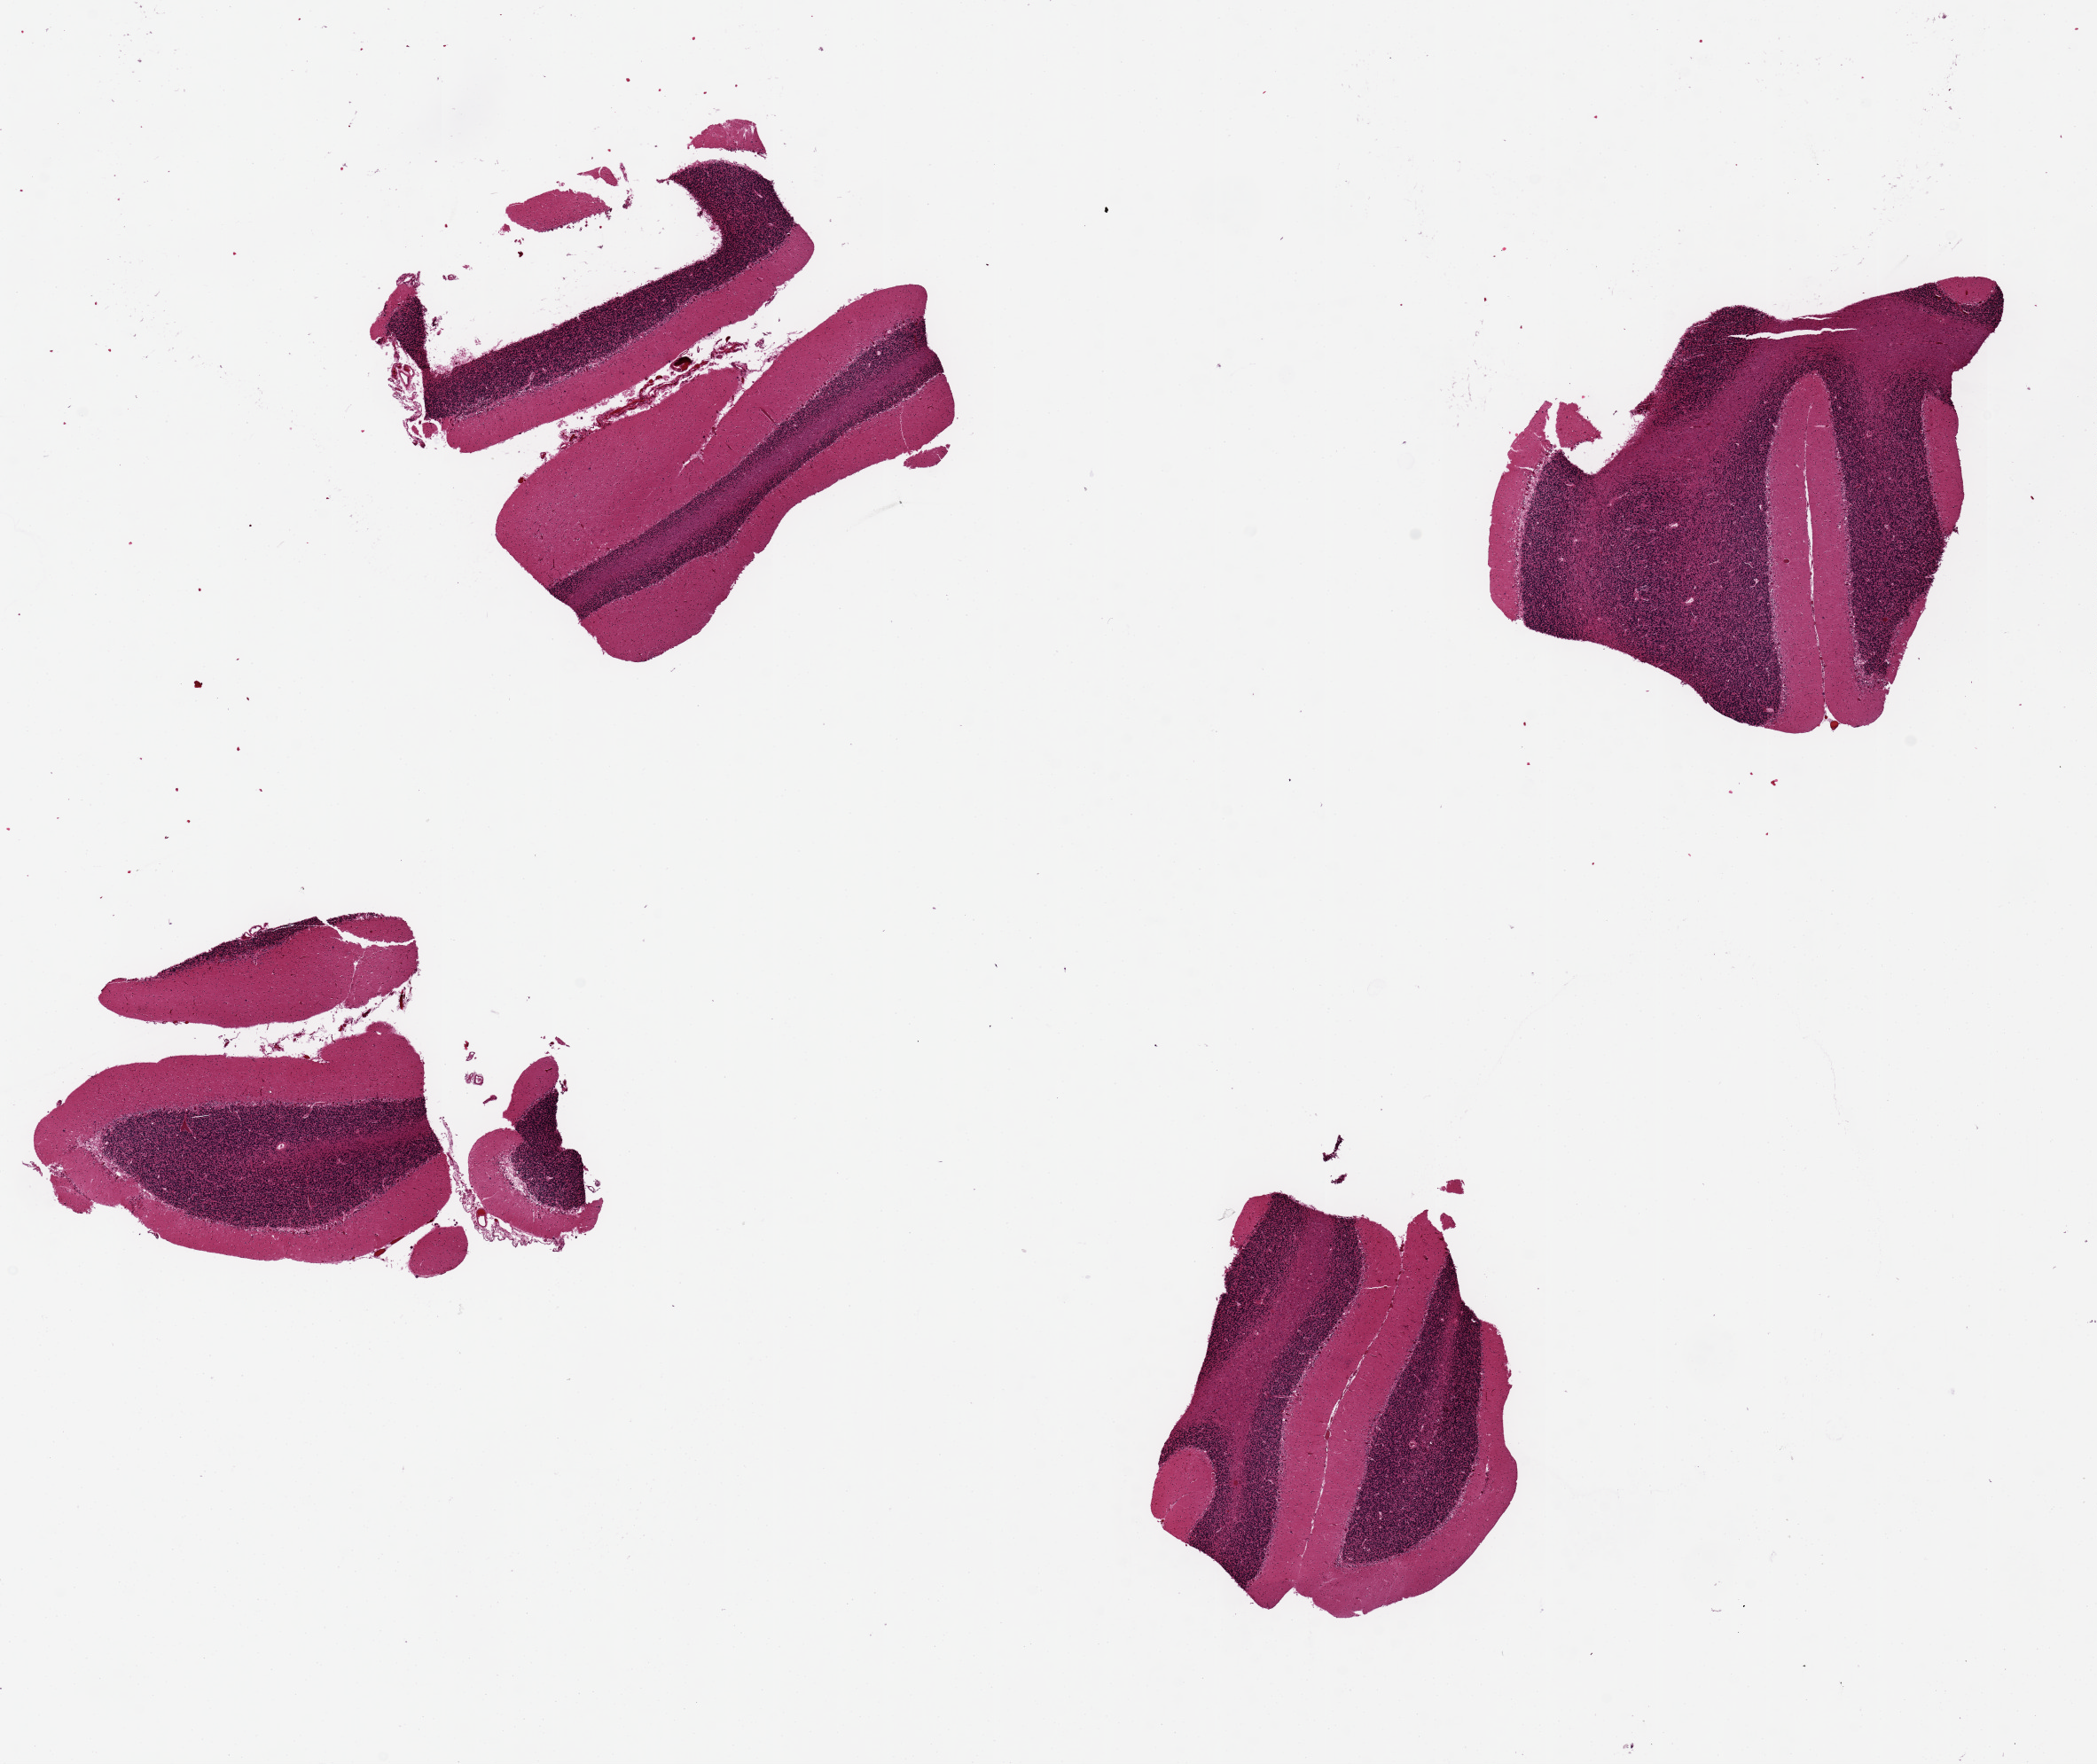
Digitized hematoxylin and eosin (H&E)-stained section, whole scanned area (about 18.7 x 15.7 mm) shown as a low-resolution overview; PAXgene-fixed, paraffin-embedded tissue; sampled site (target tissue): cerebellum; tissue donor sample. Donor: female.
Reviewer comment on this tissue sample: 4 pieces up to 4x4 mm; Purkinje nuclei faint.